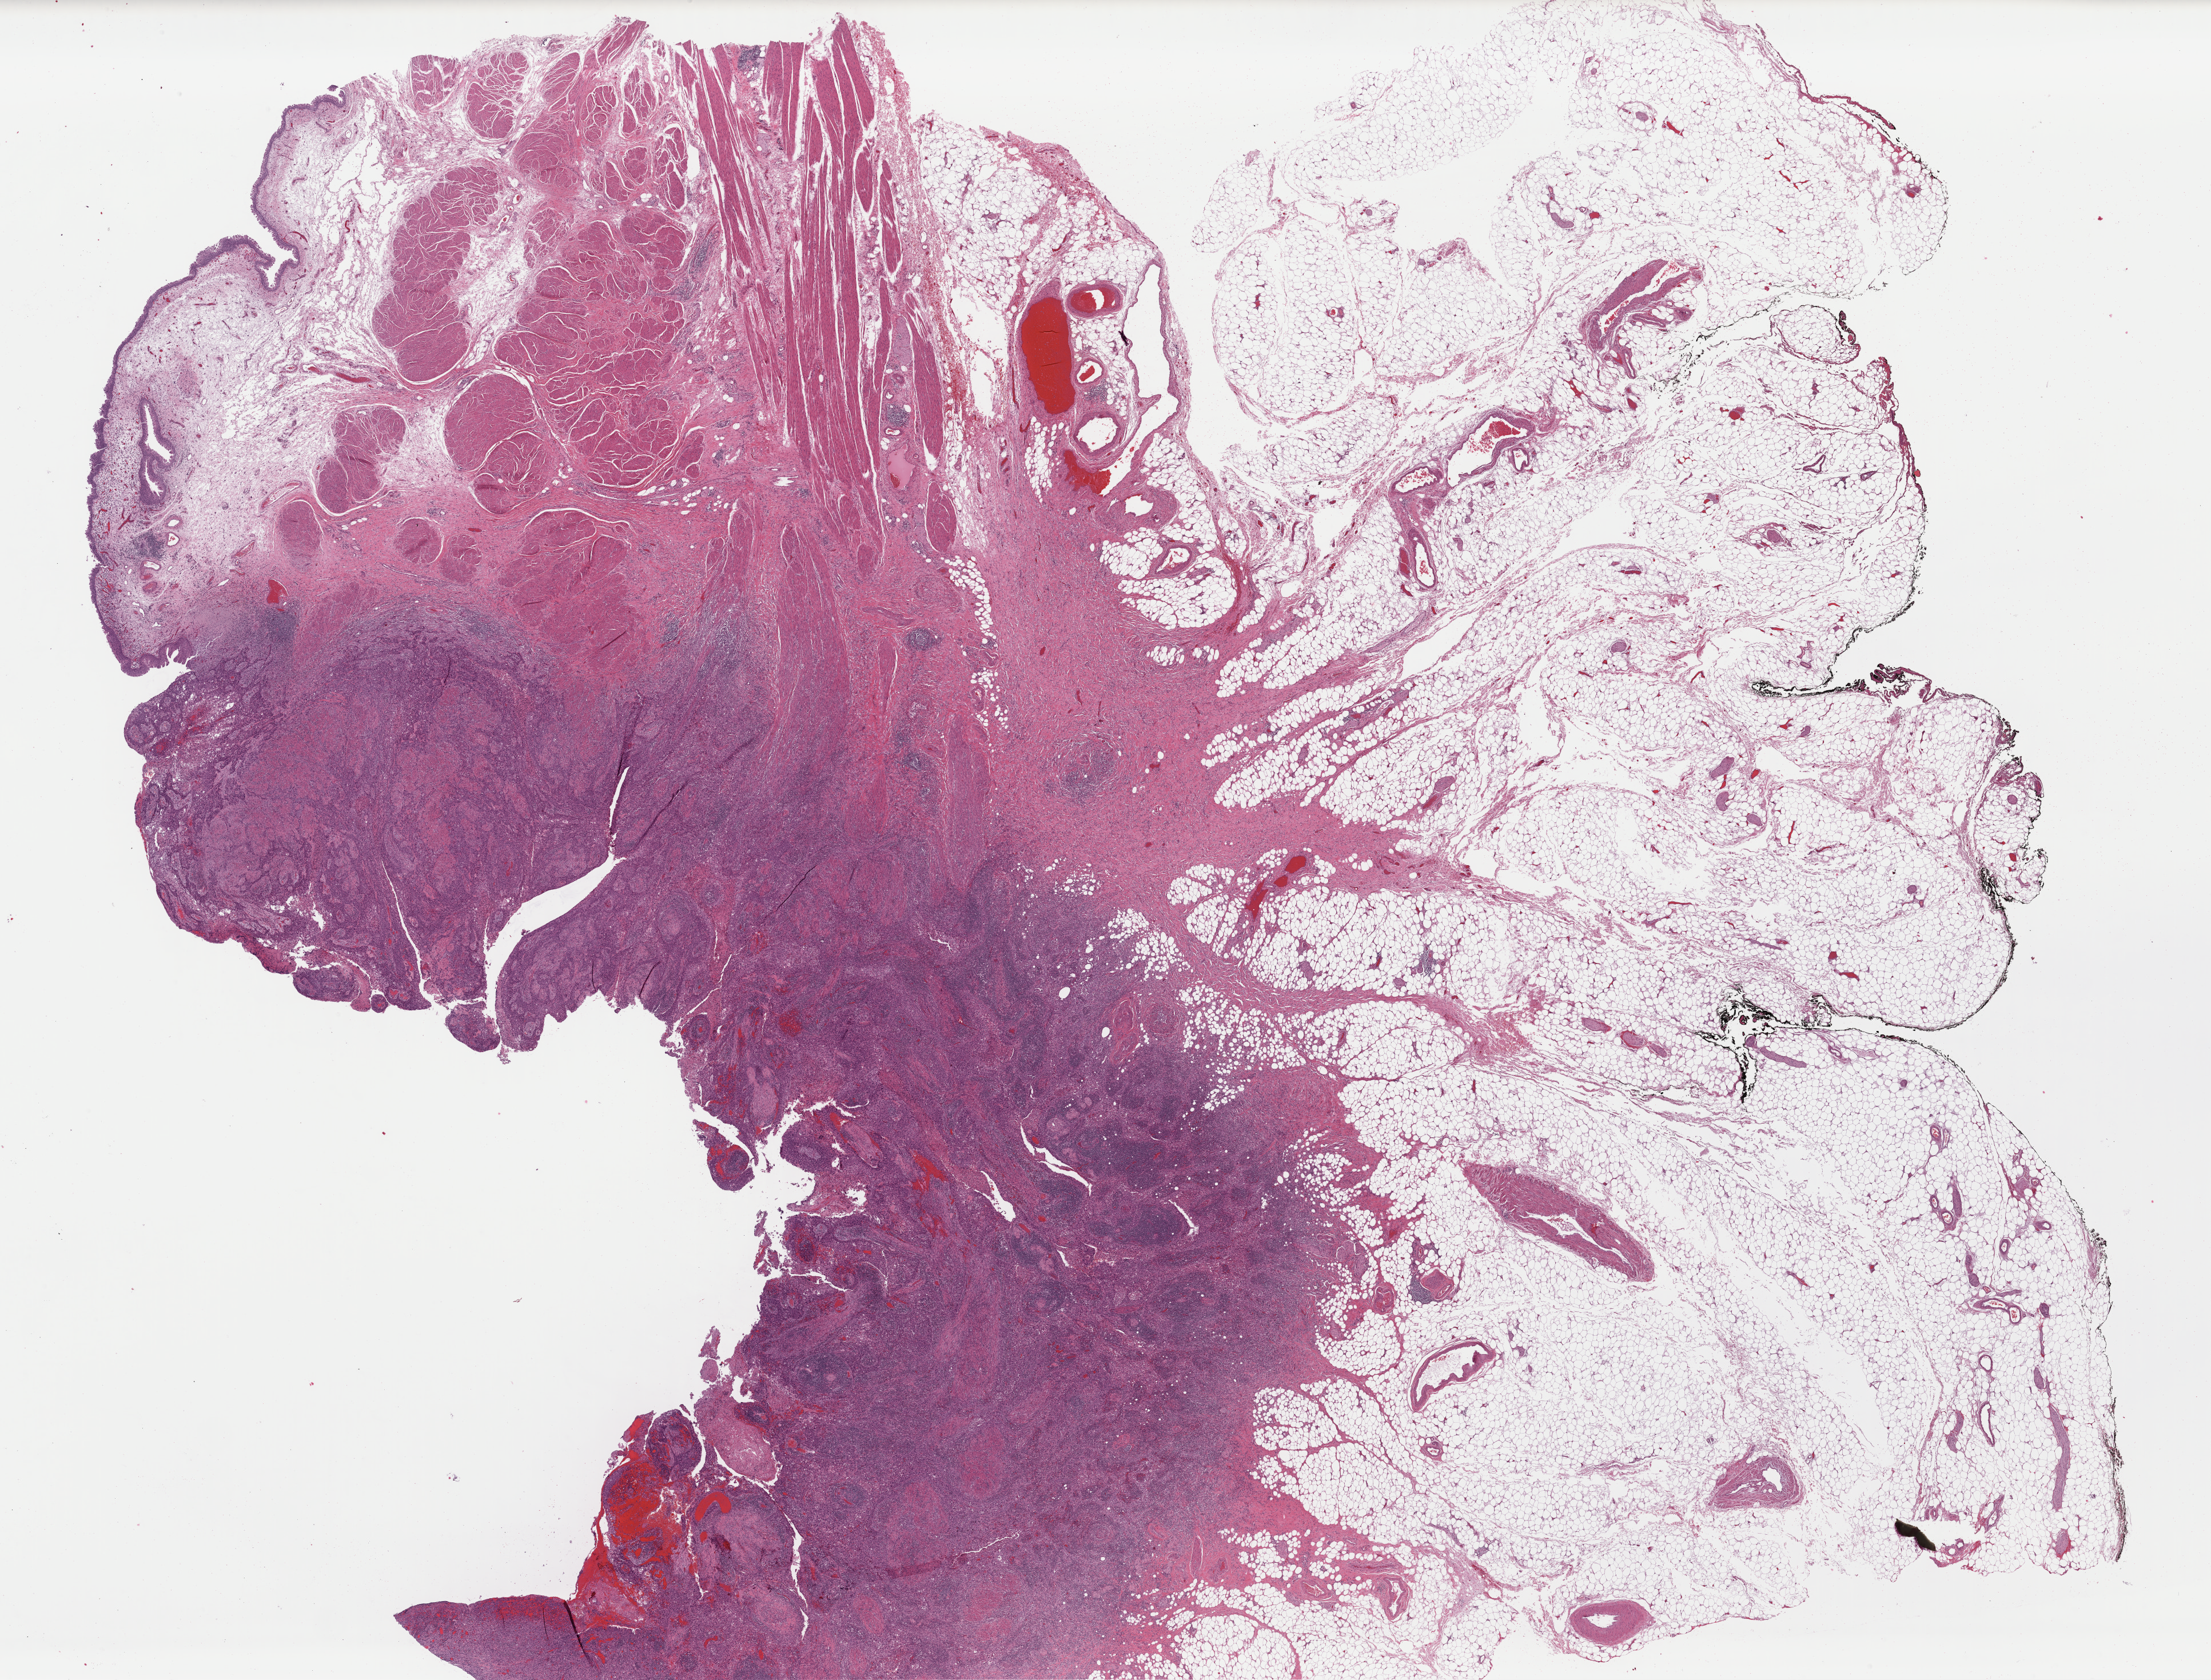
Hematoxylin and eosin (H&E) stained whole-slide image — whole scanned area (about 30.5 x 23.2 mm) shown as a low-resolution overview, formalin-fixed paraffin-embedded (FFPE) diagnostic section, bladder, primary tumour sample. Patient: female, age at initial diagnosis 74 years. Histologic grade: high grade.
- AJCC pathologic stage: III
- pathologic diagnosis: Papillary transitional cell carcinoma
- TNM: T3 N0 MX
- lymph nodes positive (case pathology): 0 of 8 examined